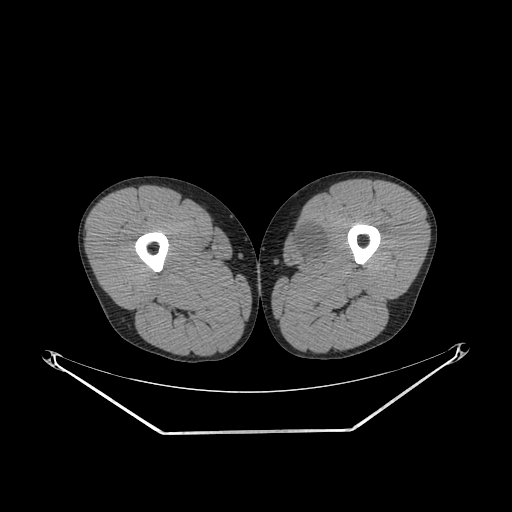
CT of an extremity soft-tissue mass (from a PET/CT study), one axial slice; slice 259 of 311 in the series (ordered by position); reconstruction kernel SOFT; soft-tissue window (W 400 / L 40 HU); 512 × 512 image matrix. Male patient. From the clinical record (not read from this slice): histological type: mixoid liposarcoma; grade: low; site of the primary tumour: left thigh.
Annotated regions visible in this slice (expert contour drawn on MRI and transferred to this co-registered scan by the dataset authors):
- gross tumour volume (mass): box from (x=292, y=226) to (x=325, y=259) px